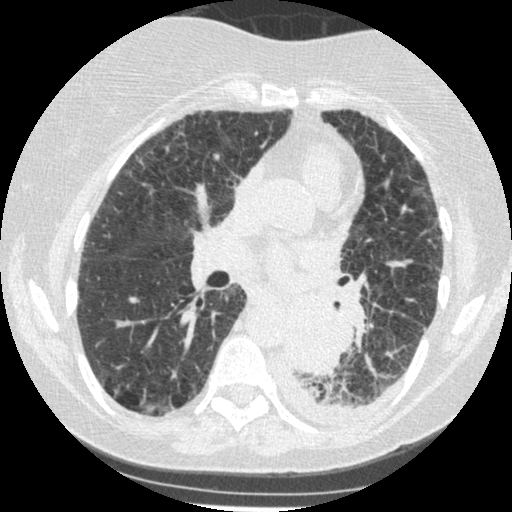
Low-dose screening chest CT, one axial slice. Position 130 of 341 along the scan axis. Reconstruction kernel STANDARD. Lung window (W 1500 / L -600 HU). 512 × 512 image matrix.
Structures marked on this image (outlined manually by an expert reader):
- lesion 1 (tumor, lower lobe of left lung): box from (x=285, y=305) to (x=347, y=376) px